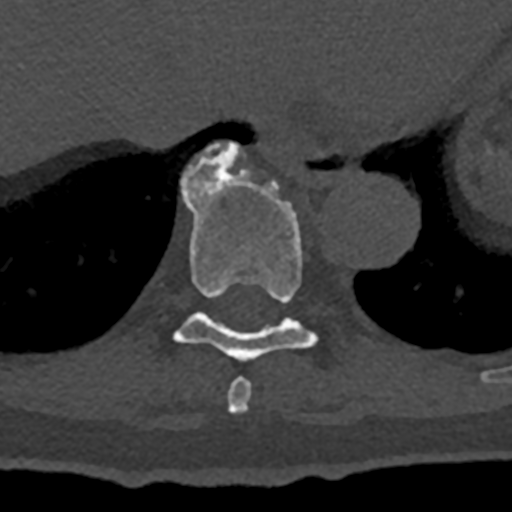
CT including the spine, one axial slice. Slice 654 of 797 in the series (ordered by position). Bone window (W 1800 / L 400 HU). 512 × 512 image matrix, field of view 160 × 160 mm. Patient: male, 74 years. From the clinical record (not read from this slice): primary cancer: renal; vertebrae with lytic lesions (as recorded): T10, L1, L2, L3, L4, L5.
Annotated regions visible in this slice (semi-automatic segmentation, software-assisted and operator-edited):
- T10 vertebra: bounding box <181,142,243,192> (left, top, right, bottom; pixels)
- T8 vertebra: <227,378,252,414>
- T9 vertebra: <173,148,318,361>